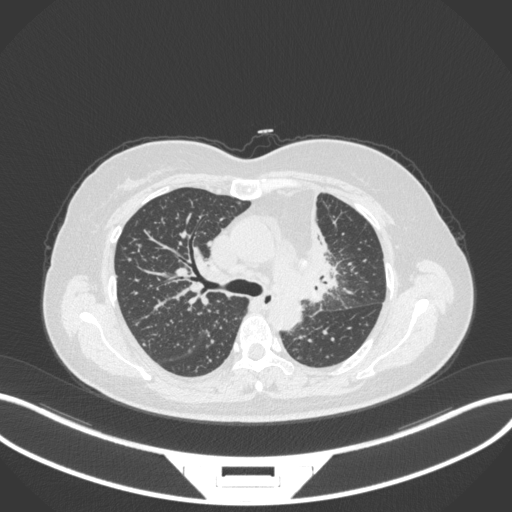
Chest CT, one axial slice. Slice 220 of 348 in the series (ordered by position). 120 kVp. Lung window (W 1500 / L -600 HU). 1 mm slice thickness. 512 × 512 image matrix, field of view 400 × 400 mm. Patient: female, 49 years. Case-level facts recorded for this patient, not image findings: clinical TNM (as recorded): T1c N0 M1.
Outlined on this slice (bounding box drawn by a radiologist):
- lung tumour (recorded histology: adenocarcinoma): box from (x=296, y=188) to (x=345, y=308) px